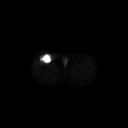
FDG PET of an extremity soft-tissue mass (from a PET/CT study), one axial slice; position 271 of 311 along the scan axis; 3.27 mm slice thickness; 128 × 128 image matrix, field of view 700 × 700 mm. Patient: male, 56 years. Case-level facts recorded for this patient, not image findings: histological type: pleiomorphic leiomyosarcoma; grade: intermediate; site of the primary tumour: right thigh.
Structures marked on this image (expert contour drawn on MRI and transferred to this co-registered scan by the dataset authors):
- gross tumour volume including surrounding oedema: bounding box [x1, y1, x2, y2] px = [39, 54, 52, 64]
- gross tumour volume (mass): [39, 54, 52, 64]